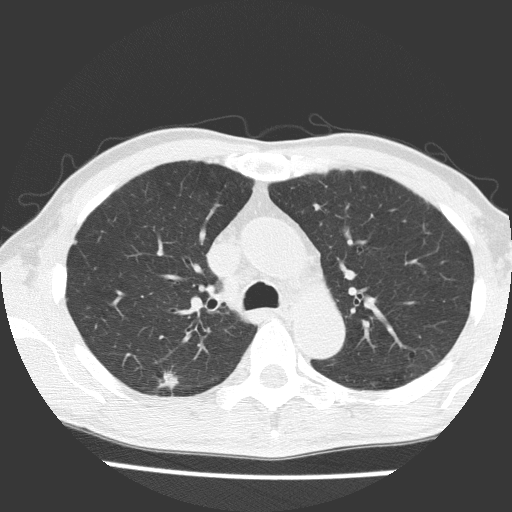
Low-dose screening chest CT, one axial slice. Slice 112 of 160 in the series (ordered by position). Reconstruction kernel FC51. 120 kVp. Lung window (W 1500 / L -600 HU). 2 mm slice thickness. 512 × 512 image matrix, field of view 309 × 309 mm.
Outlined on this slice (manually delineated by an expert):
- lesion 1 (tumor, upper lobe of right lung): bounding box (x1, y1, x2, y2) in pixels: (158, 371, 179, 390)